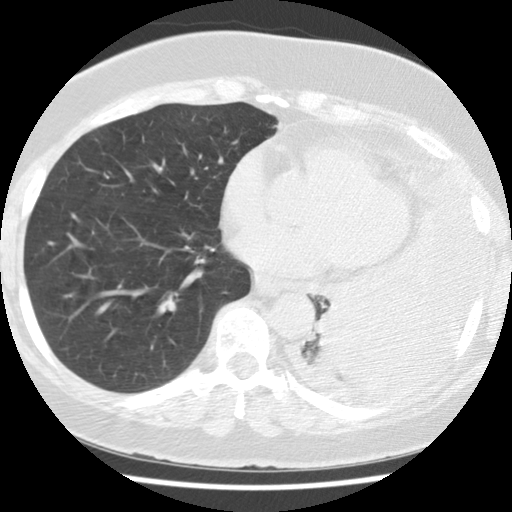
Low-dose screening chest CT, axial slice. First (baseline) screen. Lung window (W 1500 / L -600 HU). 2.5 mm slice thickness. Slice 70 of 114 in the series. 512 × 512 image matrix. Female, age 65 years at enrolment.
Expert-annotated lung lesion, bounding box (x1, y1, x2, y2) in pixels: (314, 281, 436, 385). The exam's reader record, not a measurement of the box and not confirmed to be the same lesion: non-calcified nodule or mass ≥4 mm, left lower lobe, 74 × 48 mm, spiculated (stellate) margins, soft tissue attenuation. Official screen result: positive, change unspecified: nodule(s) >= 4 mm or enlarging nodule(s), mass(es), or other non-specific abnormalities suspicious for lung cancer. Later outcome: lung cancer diagnosed 13 days after this screen — adenocarcinoma, NOS, left lower lobe, stage IV (AJCC 6th edition), 74 mm at pathology.